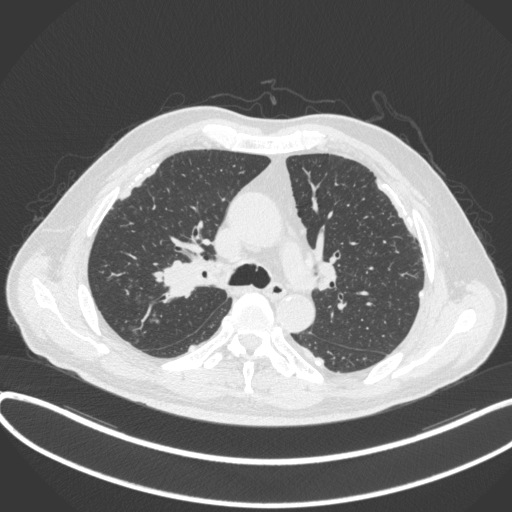
Chest CT, one axial slice; reconstruction kernel B31f; lung window (W 1500 / L -600 HU); 1 mm slice thickness; 512 × 512 image matrix, field of view 400 × 400 mm. Patient: male, 58 years. From the clinical record (not read from this slice): clinical TNM (as recorded): T1c N0 M0.
Structures marked on this image (rectangle marked by the reading radiologist):
- lung tumour (recorded histology: squamous cell carcinoma): bounding box (x1, y1, x2, y2) in pixels: (151, 253, 205, 303)